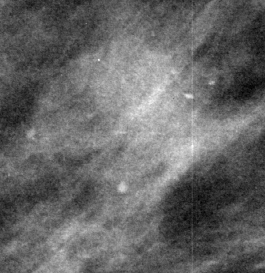
Region of interest cut from a scanned film mammogram (one marked finding); right breast; MLO view.
Calcifications, morphology punctate / pleomorphic, distribution clustered; BI-RADS assessment category 3; subtlety rating 3 on a 1 (subtle) to 5 (obvious) scale; pathology result (as recorded, not read from the image): benign.